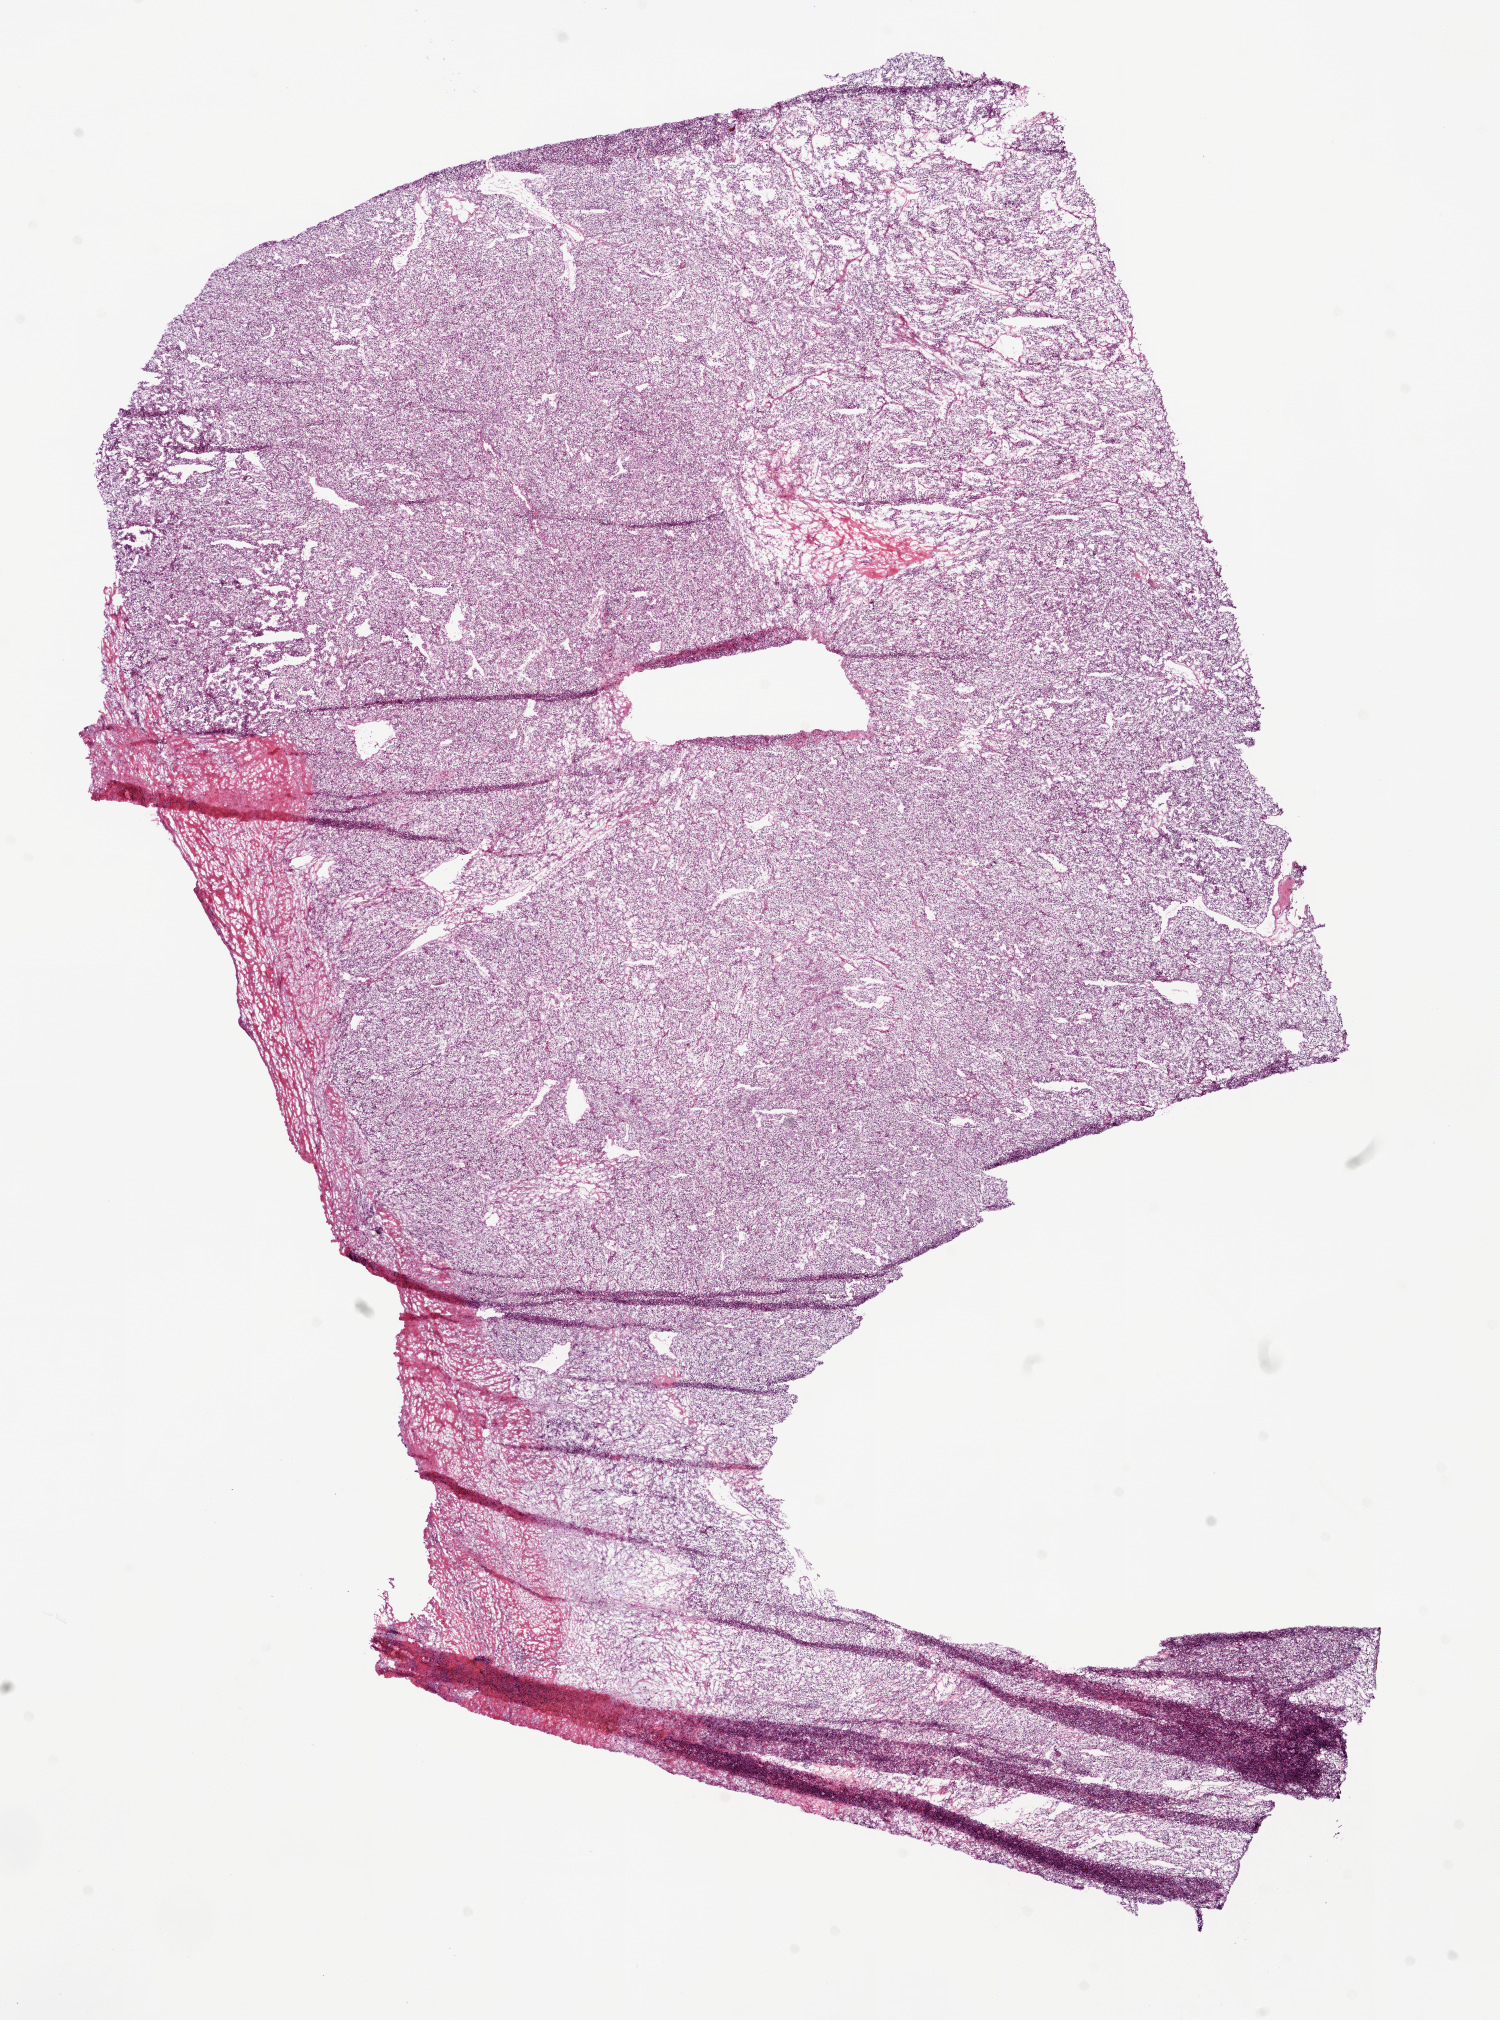
Whole-slide histology image, H&E, low-resolution overview of the scanned area, about 12.0 x 16.2 mm, frozen section from the bottom of the tissue portion, sample: primary tumour, kidney. Male, age 42 years at initial diagnosis. Histologic grade: G2 (moderately differentiated). Slide review estimates, as recorded: tumour cells 95%, tumour nuclei 85%, normal cells 0%, stromal cells 5%, necrosis 0%.
- laterality: right
- histologic diagnosis: Clear cell adenocarcinoma, NOS
- AJCC pathologic stage: II